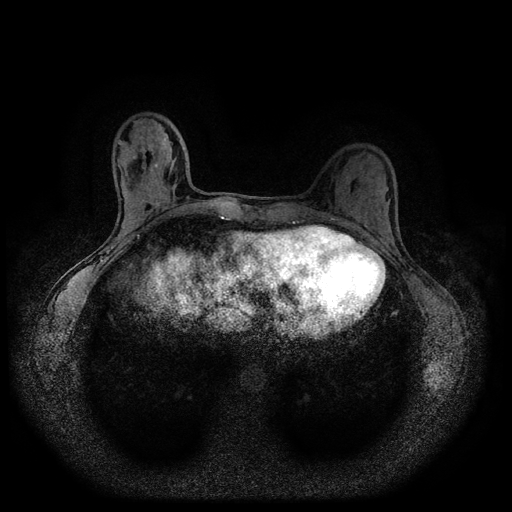
Breast MRI (dynamic contrast-enhanced, multi-phase), one axial slice; slice 35 of 116 in the series (ordered by position); dynamic contrast-enhanced series, time point 2 of 5 at this slice position (early post-contrast); 1.5 T; TE 2.7 ms, TR 5.4 ms; 2 mm slice thickness; 512 × 512 image matrix, field of view 330 × 330 mm. Patient: female, 32 years.
Annotated regions visible in this slice (semi-automatic segmentation, software-assisted and operator-edited):
- breast lesion (labelled benign in the annotation): bounding box (x1, y1, x2, y2) in pixels: (126, 148, 138, 163)